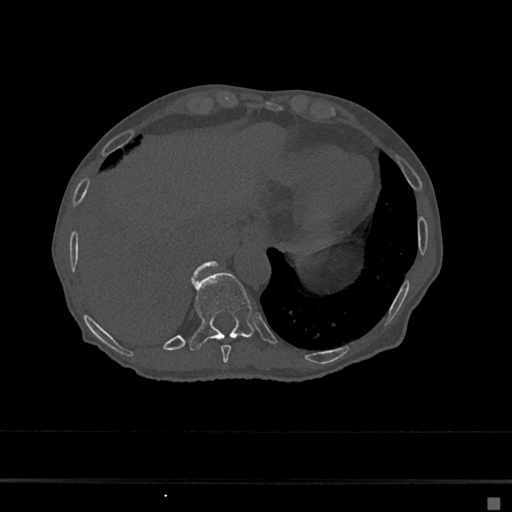
CT including the spine, one axial slice; position 234 of 797 along the scan axis; 120 kVp; bone window (W 1800 / L 400 HU); 512 × 512 image matrix, field of view 360 × 360 mm. Female patient, age 68 years. From the clinical record (not read from this slice): primary cancer: renal.
Annotated regions visible in this slice (semi-automatic segmentation, software-assisted and operator-edited):
- T10 vertebra: bounding box (x1, y1, x2, y2) in pixels: (189, 272, 256, 350)
- T11 vertebra: (192, 261, 217, 279)
- T9 vertebra: (221, 345, 232, 363)